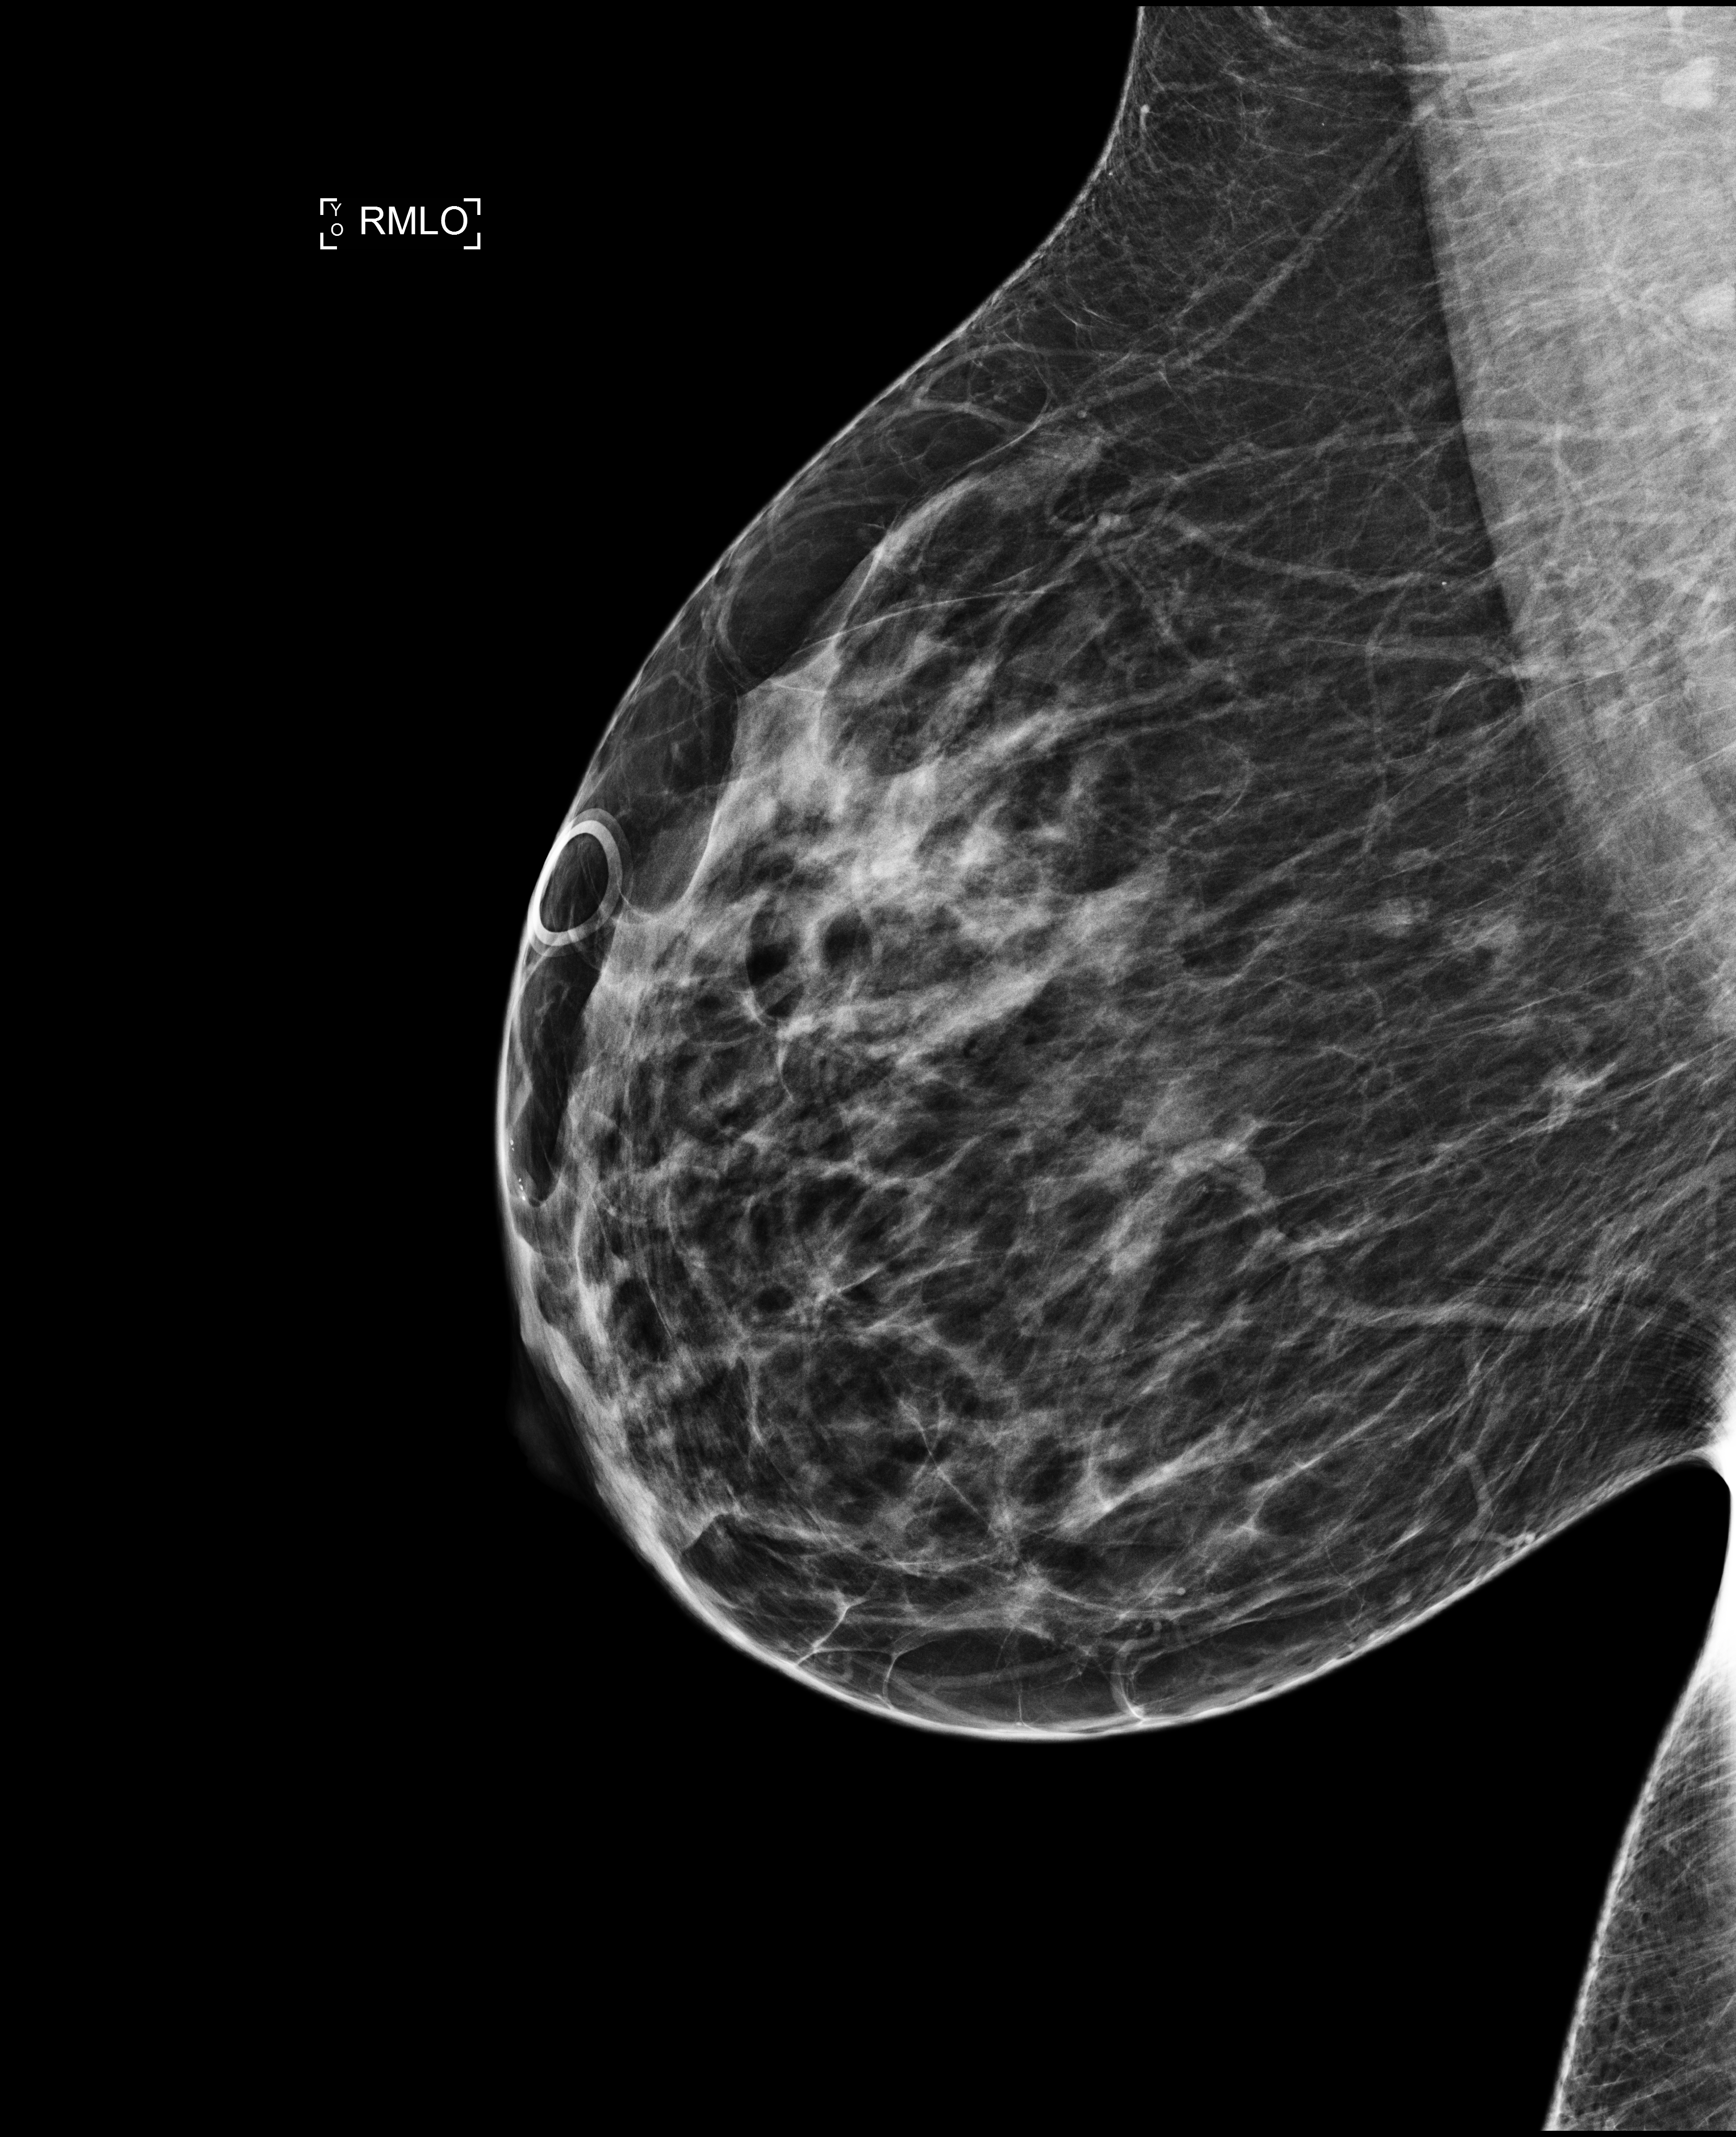
Full-field digital mammogram (FFDM); right breast; medio-lateral oblique projection; screening examination; compressed breast thickness 58 mm. Patient: female, 46 years.
Breast density at the screening exam (both breasts): heterogeneously dense (BI-RADS density category c). Final BI-RADS category for the screening round (tomosynthesis exam, both breasts): category 2. Recall: recalled for additional imaging after this screen.